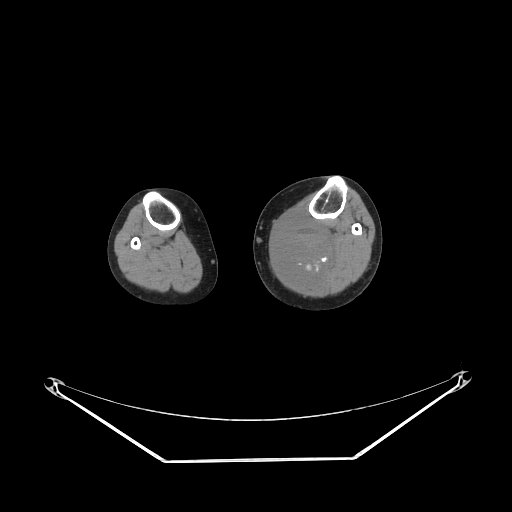
CT of an extremity soft-tissue mass (from a PET/CT study), one axial slice. Slice 150 of 223 in the series (ordered by position). Soft-tissue window (W 400 / L 40 HU). 512 × 512 image matrix, field of view 500 × 500 mm. Female patient. Case-level facts recorded for this patient, not image findings: histological type: extraskeletal high grade osteogenic sarcoma; grade: high; site of the primary tumour: left calf.
Structures marked on this image (expert contour drawn on MRI and transferred to this co-registered scan by the dataset authors):
- gross tumour volume (mass): bounding box (x1, y1, x2, y2) in pixels: (272, 217, 337, 282)